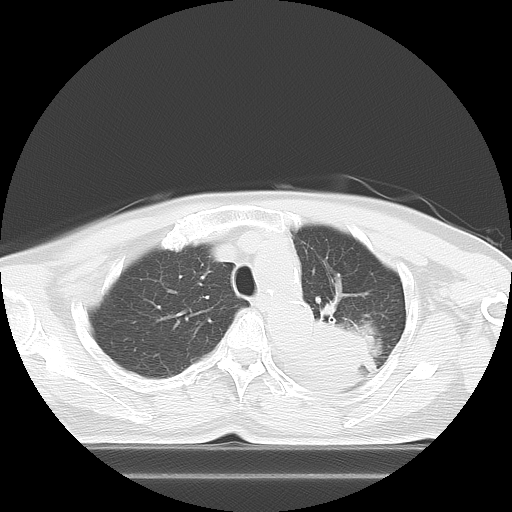
Chest CT, one axial slice; slice 9 of 21 in the series (ordered by position); 120 kVp; lung window (W 1500 / L -600 HU); 5 mm slice thickness; 512 × 512 image matrix, field of view 350 × 350 mm. Patient: female, 74 years. From the clinical record (not read from this slice): clinical TNM (as recorded): T3 N1 M1c.
Outlined on this slice (bounding box drawn by a radiologist):
- lung tumour (recorded histology: small cell carcinoma): box from (x=296, y=310) to (x=382, y=389) px